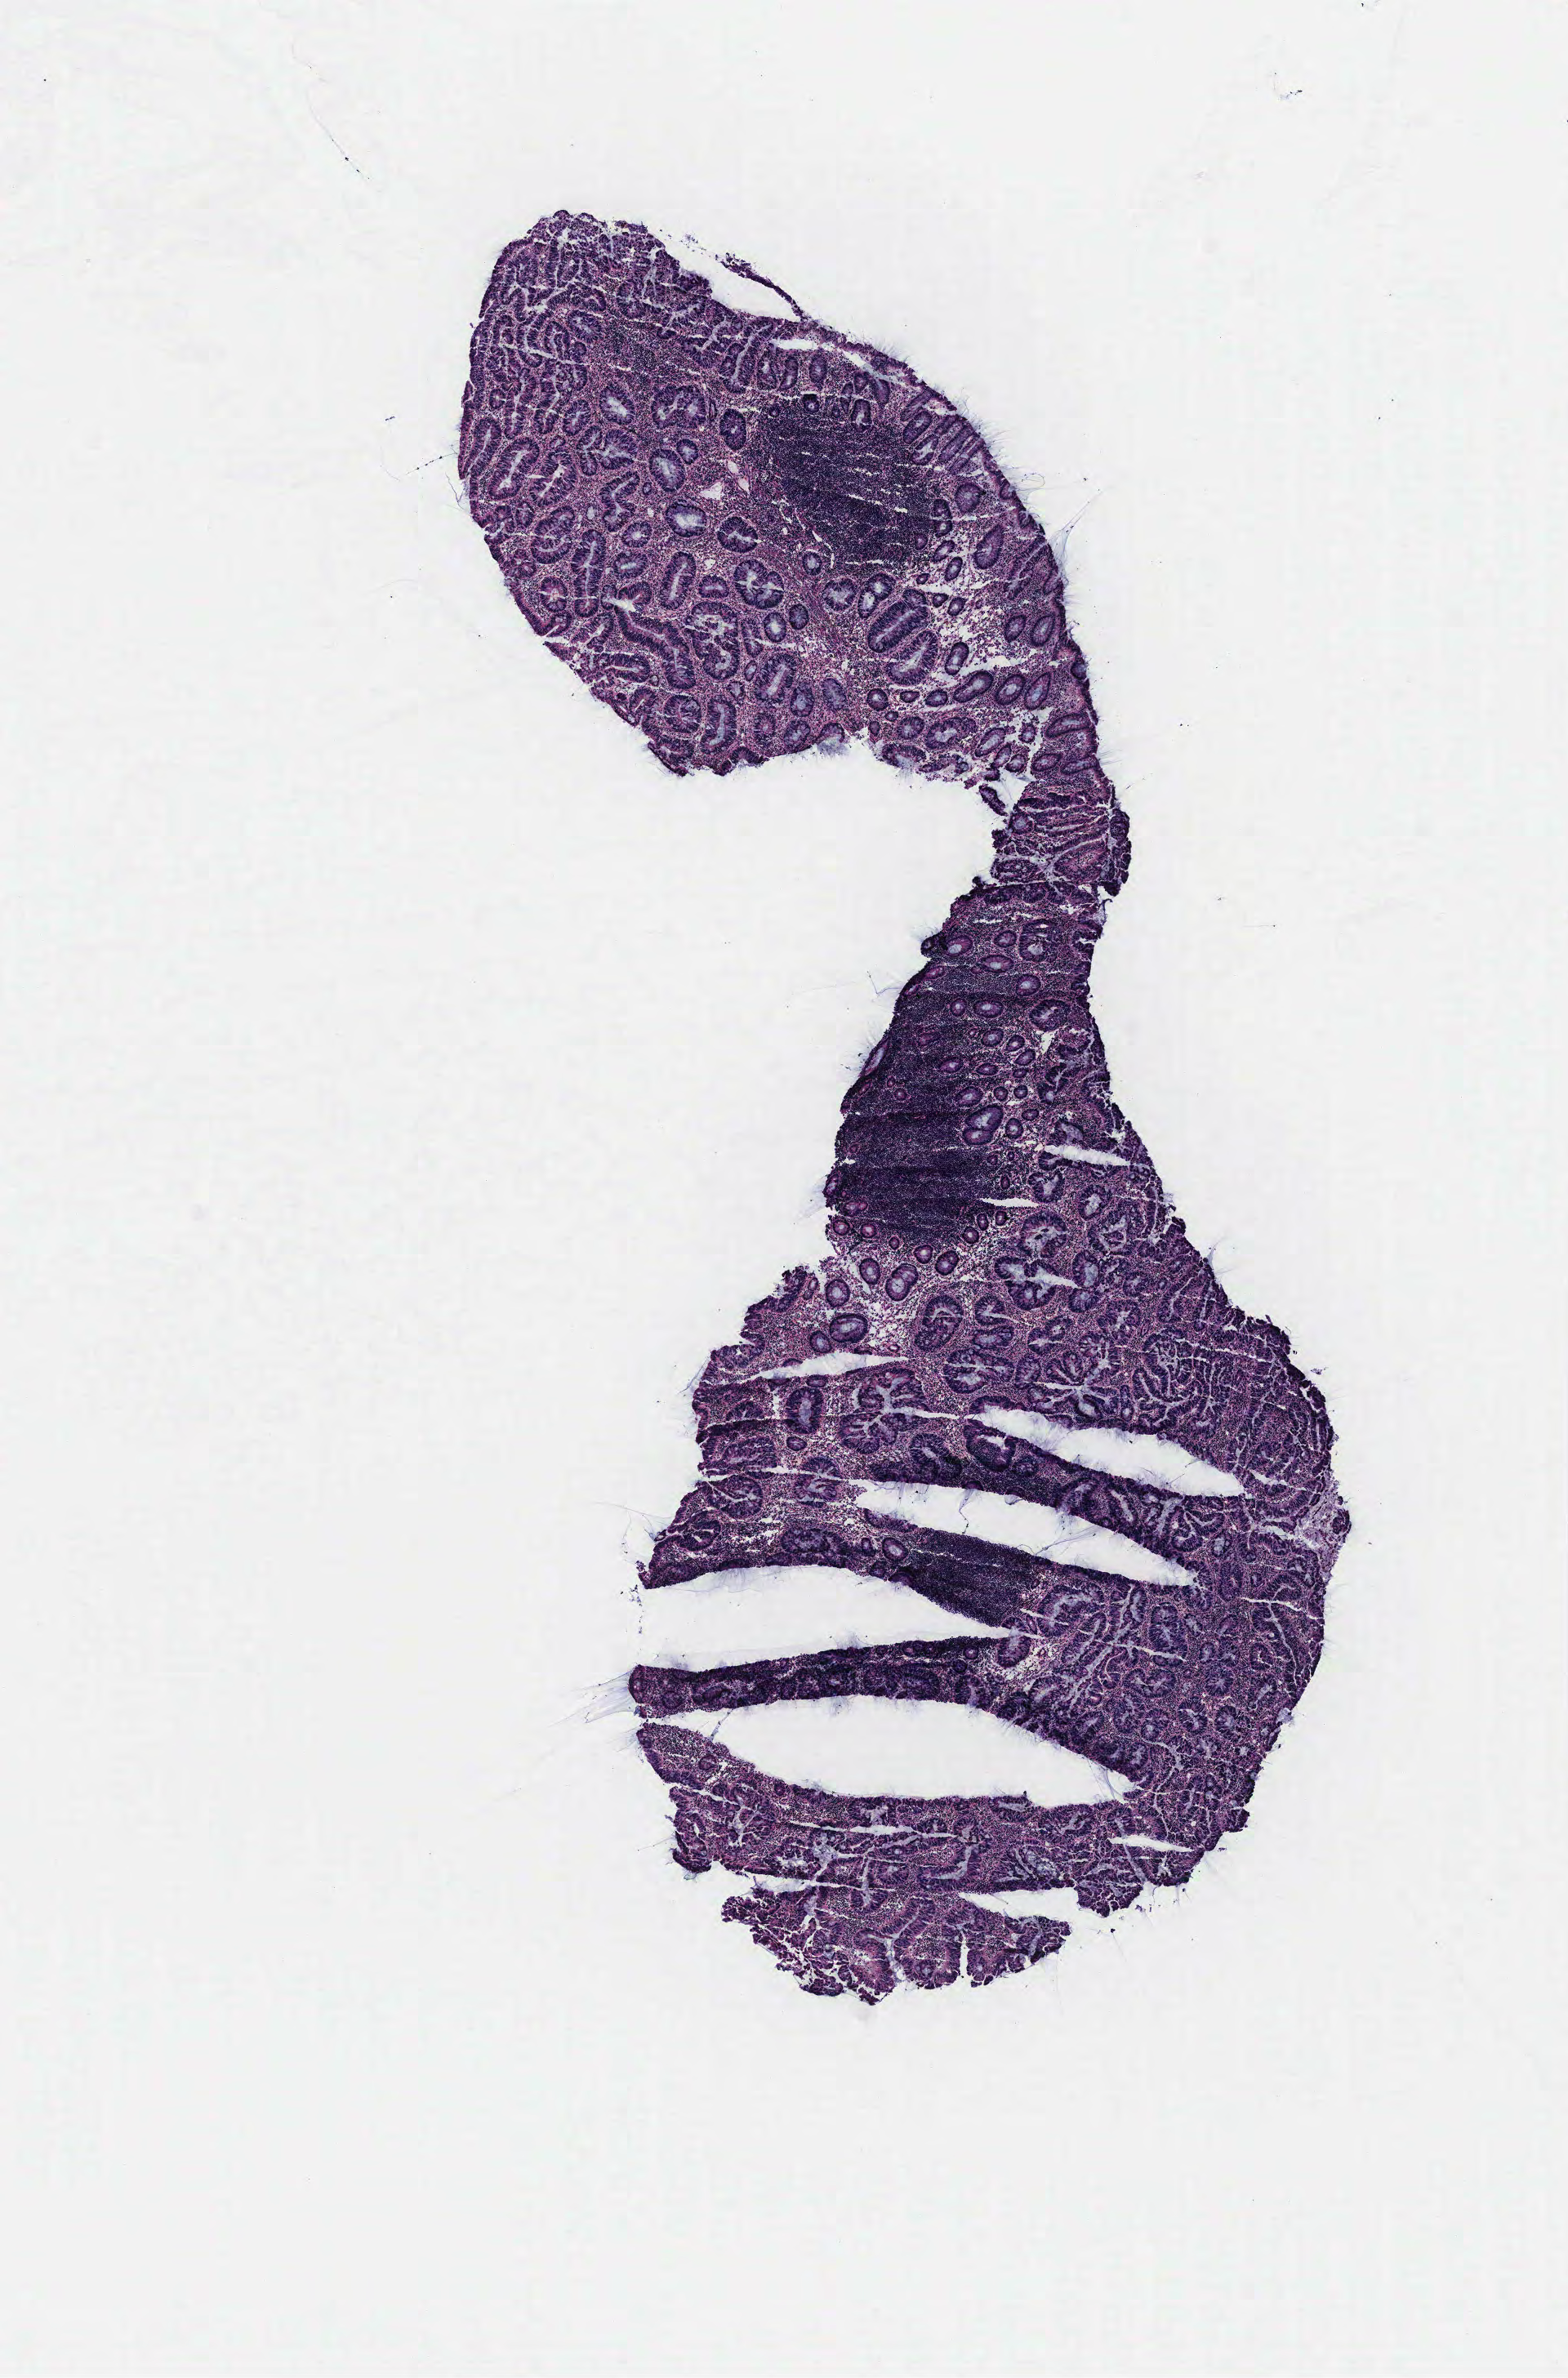
Whole-slide histology image, H&E-stained, whole scanned area (about 7.7 x 11.7 mm, slide scanned at 40x) shown as a low-resolution overview; colon, tissue type not recorded. Patient sex: female.
Patient diagnosis: Adenocarcinoma, NOS.